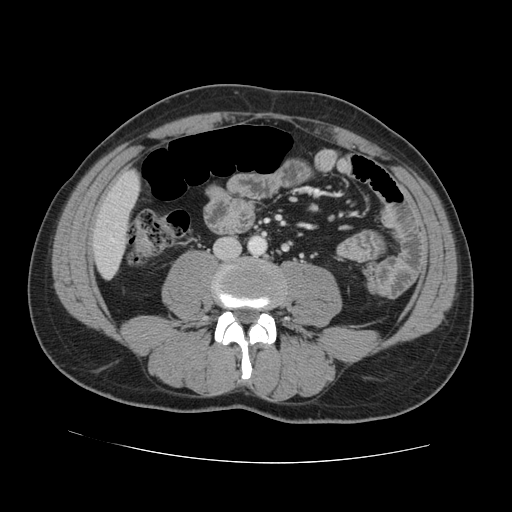
Contrast-enhanced abdominal CT, one axial slice. 120 kVp. Intravenous contrast given. Soft-tissue window (W 400 / L 40 HU). 2.5 mm slice thickness. 512 × 512 image matrix, field of view 380 × 380 mm. Male patient, age 40 years. Case-level facts recorded for this patient, not image findings: diagnosis: colorectal cancer liver metastases, imaged before liver resection; multiple liver metastases: yes; largest metastasis: 2.9 cm.
Annotated regions visible in this slice (expert manual segmentation):
- liver: bounding box <94,173,138,276> (left, top, right, bottom; pixels)